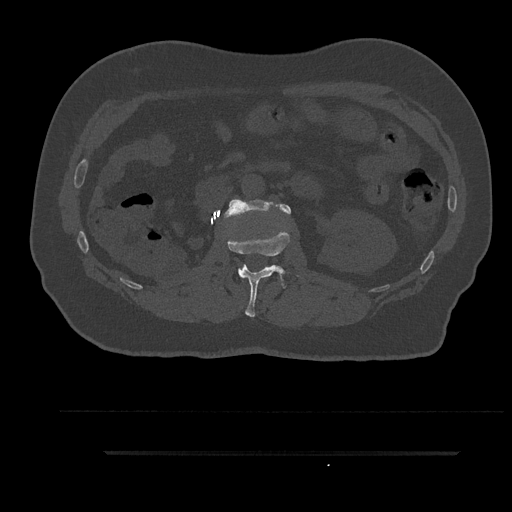
CT including the spine, one axial slice; slice 157 of 797 in the series (ordered by position); reconstruction kernel Br40s/3; 120 kVp; bone window (W 1800 / L 400 HU); 0.5 mm slice thickness; 512 × 512 image matrix, field of view 432 × 432 mm. Male patient, age 63 years. Case-level facts recorded for this patient, not image findings: primary cancer: renal; vertebrae with lytic lesions (as recorded): T8.
Structures marked on this image (semi-automatic segmentation, software-assisted and operator-edited):
- L1 vertebra: bounding box <227,230,298,317> (left, top, right, bottom; pixels)
- L2 vertebra: <224,199,291,218>